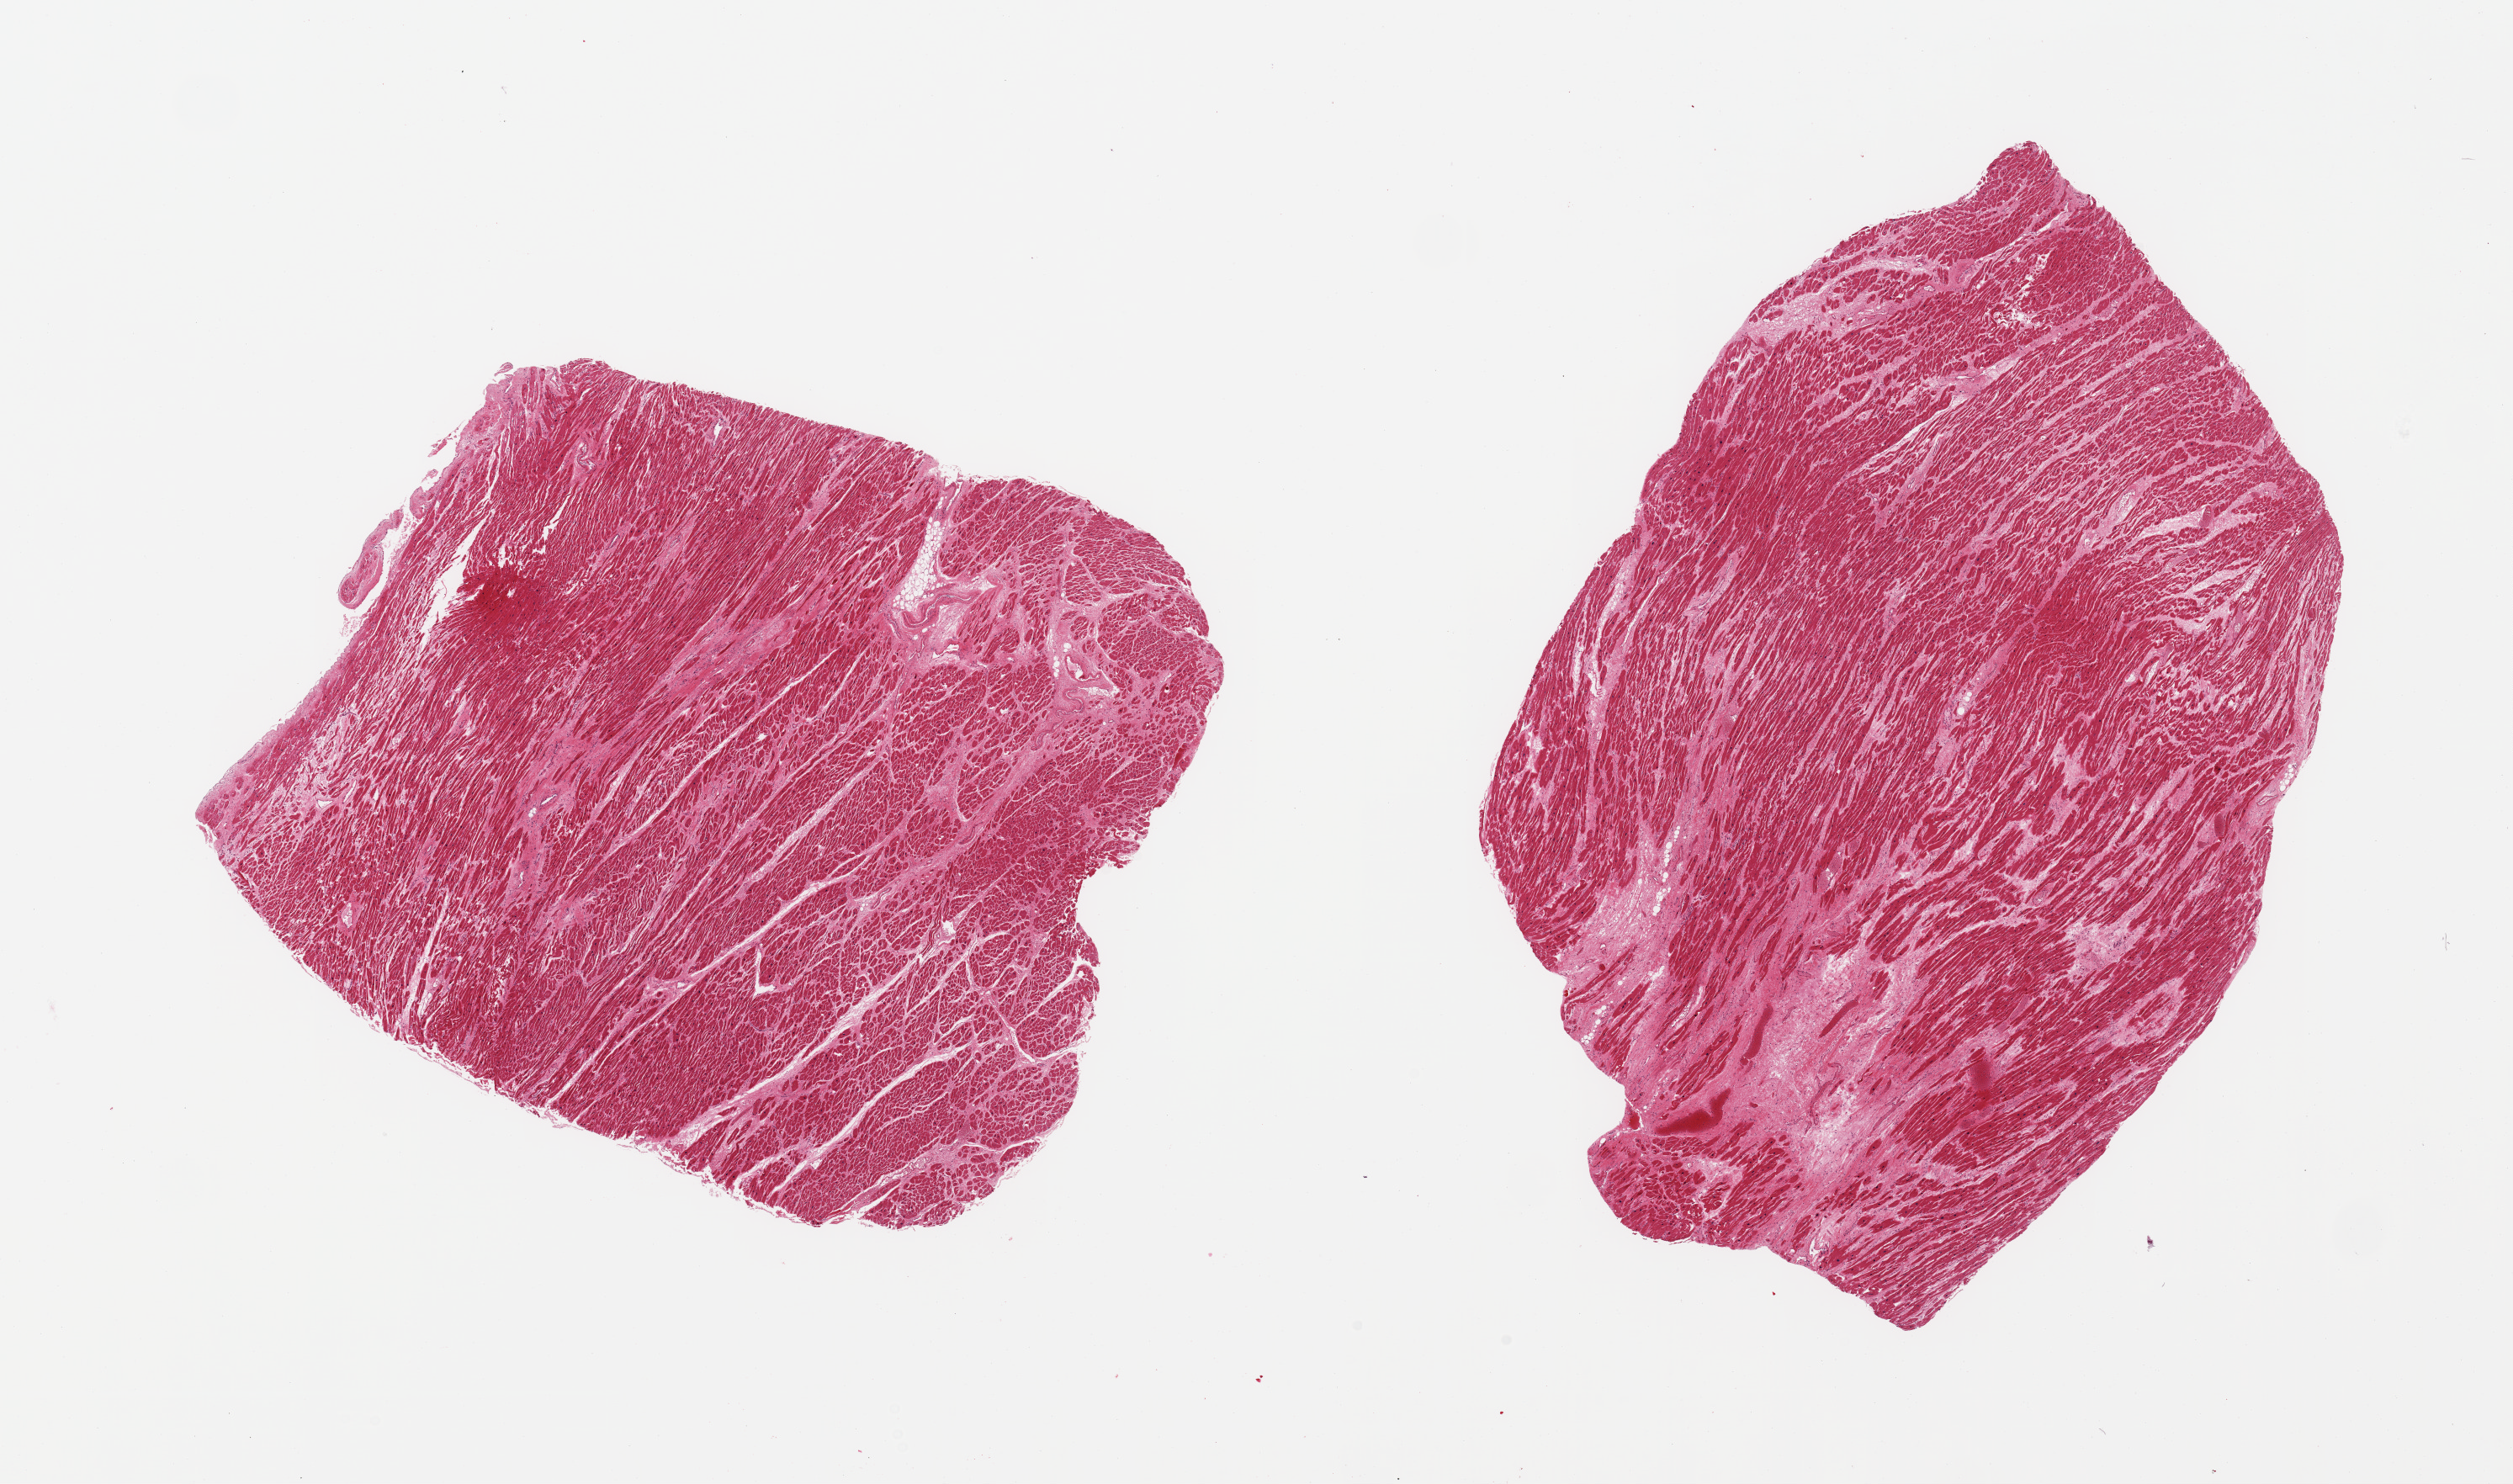
Whole-slide image, haematoxylin and eosin stain, brightfield — shown as a low-resolution overview of the whole scanned area (about 23.6 x 14.0 mm, slide scanned at 20x); PAXgene-fixed paraffin-embedded (PFPE) section; section of heart (target tissue); donor tissue sample. Donor sex: male.
* reviewer comment on this tissue sample: 2 pieces, moderate/marked interstitial fibrosis/chronic ischemic change; ~3mm remote infarct